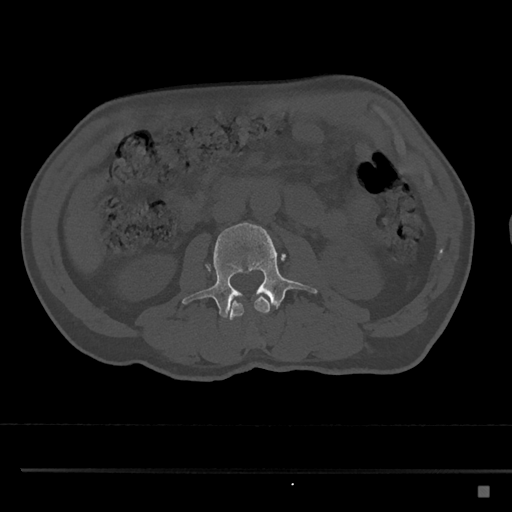
CT including the spine, one axial slice; slice 713 of 797 in the series (ordered by position); 120 kVp; bone window (W 1800 / L 400 HU); 512 × 512 image matrix, field of view 391 × 391 mm. Male patient, age 59 years. Case-level facts recorded for this patient, not image findings: primary cancer: prostate.
Outlined on this slice (semi-automatically segmented with operator editing):
- L2 vertebra: box from (x=228, y=295) to (x=270, y=320) px
- L3 vertebra: (x=182, y=222)–(x=318, y=318)